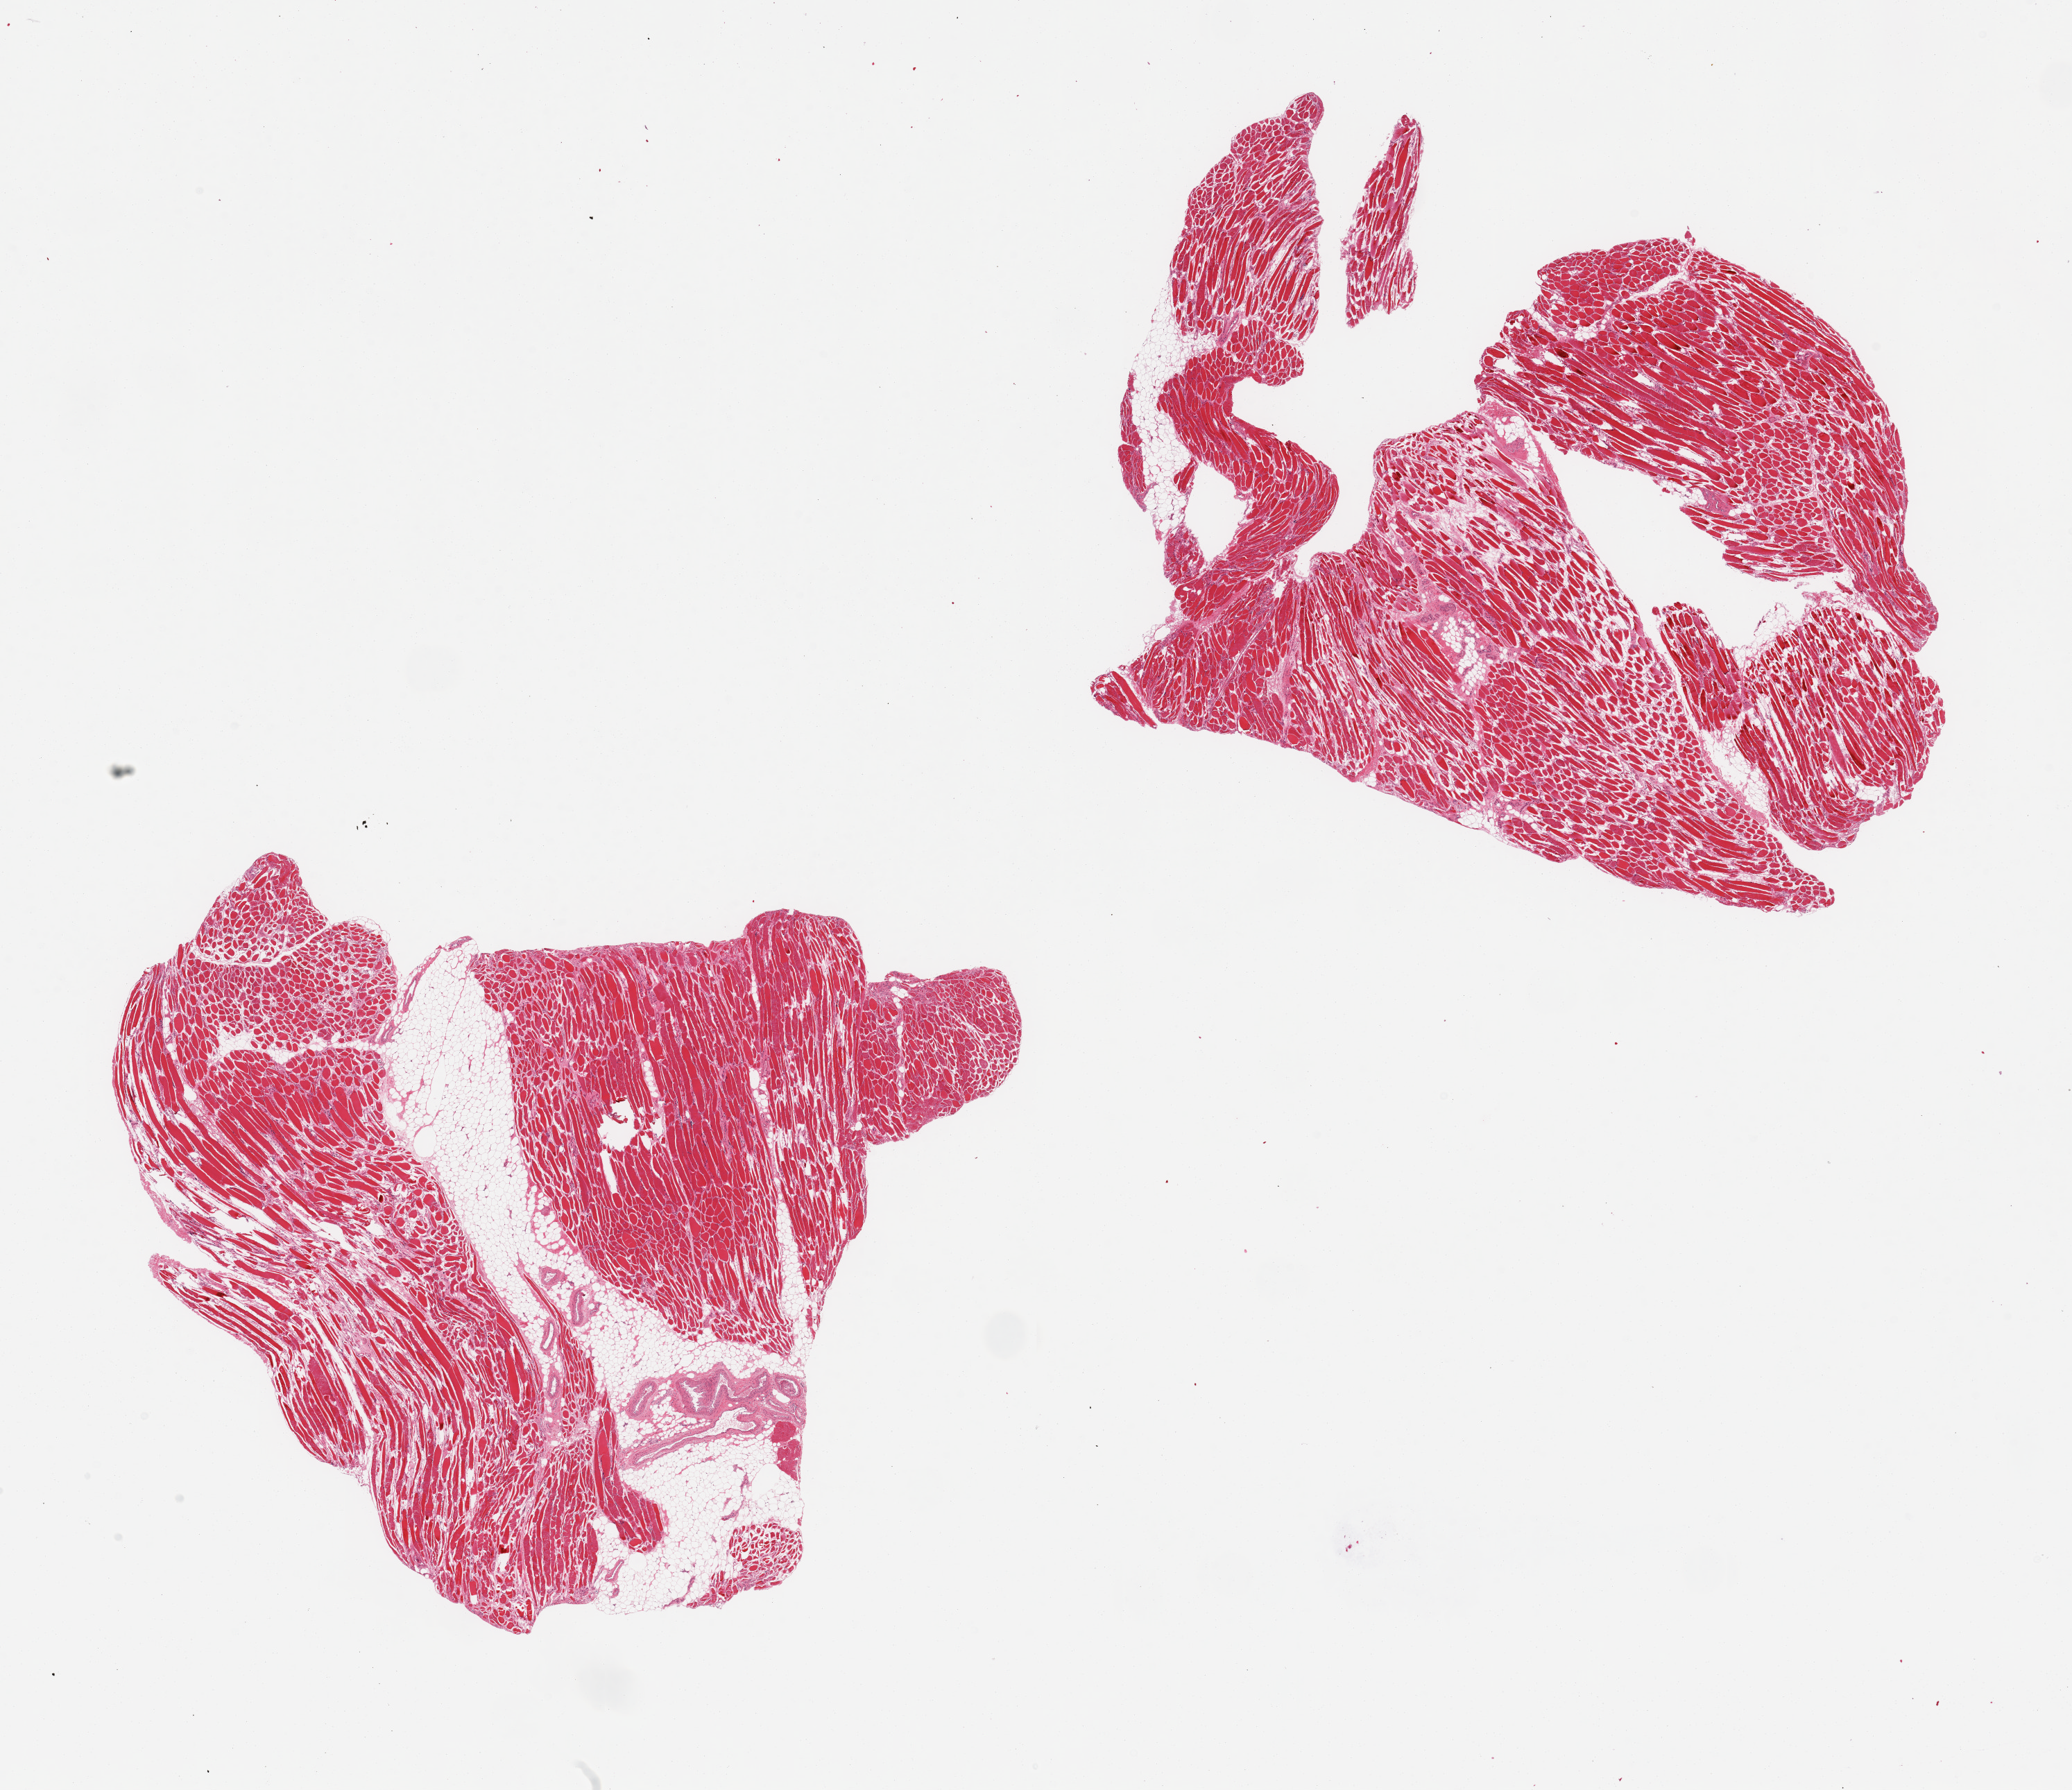
Digitized haematoxylin and eosin-stained section — a low-resolution overview of the entire scanned area, about 23.6 x 20.4 mm, PAXgene-fixed, paraffin-embedded tissue, section of skeletal muscle (target tissue), tissue donor sample. Donor sex: male.
• pathologist's review note for this sample: 2 pieces; focal atrophy with fiber drop-out and to 20% fat content